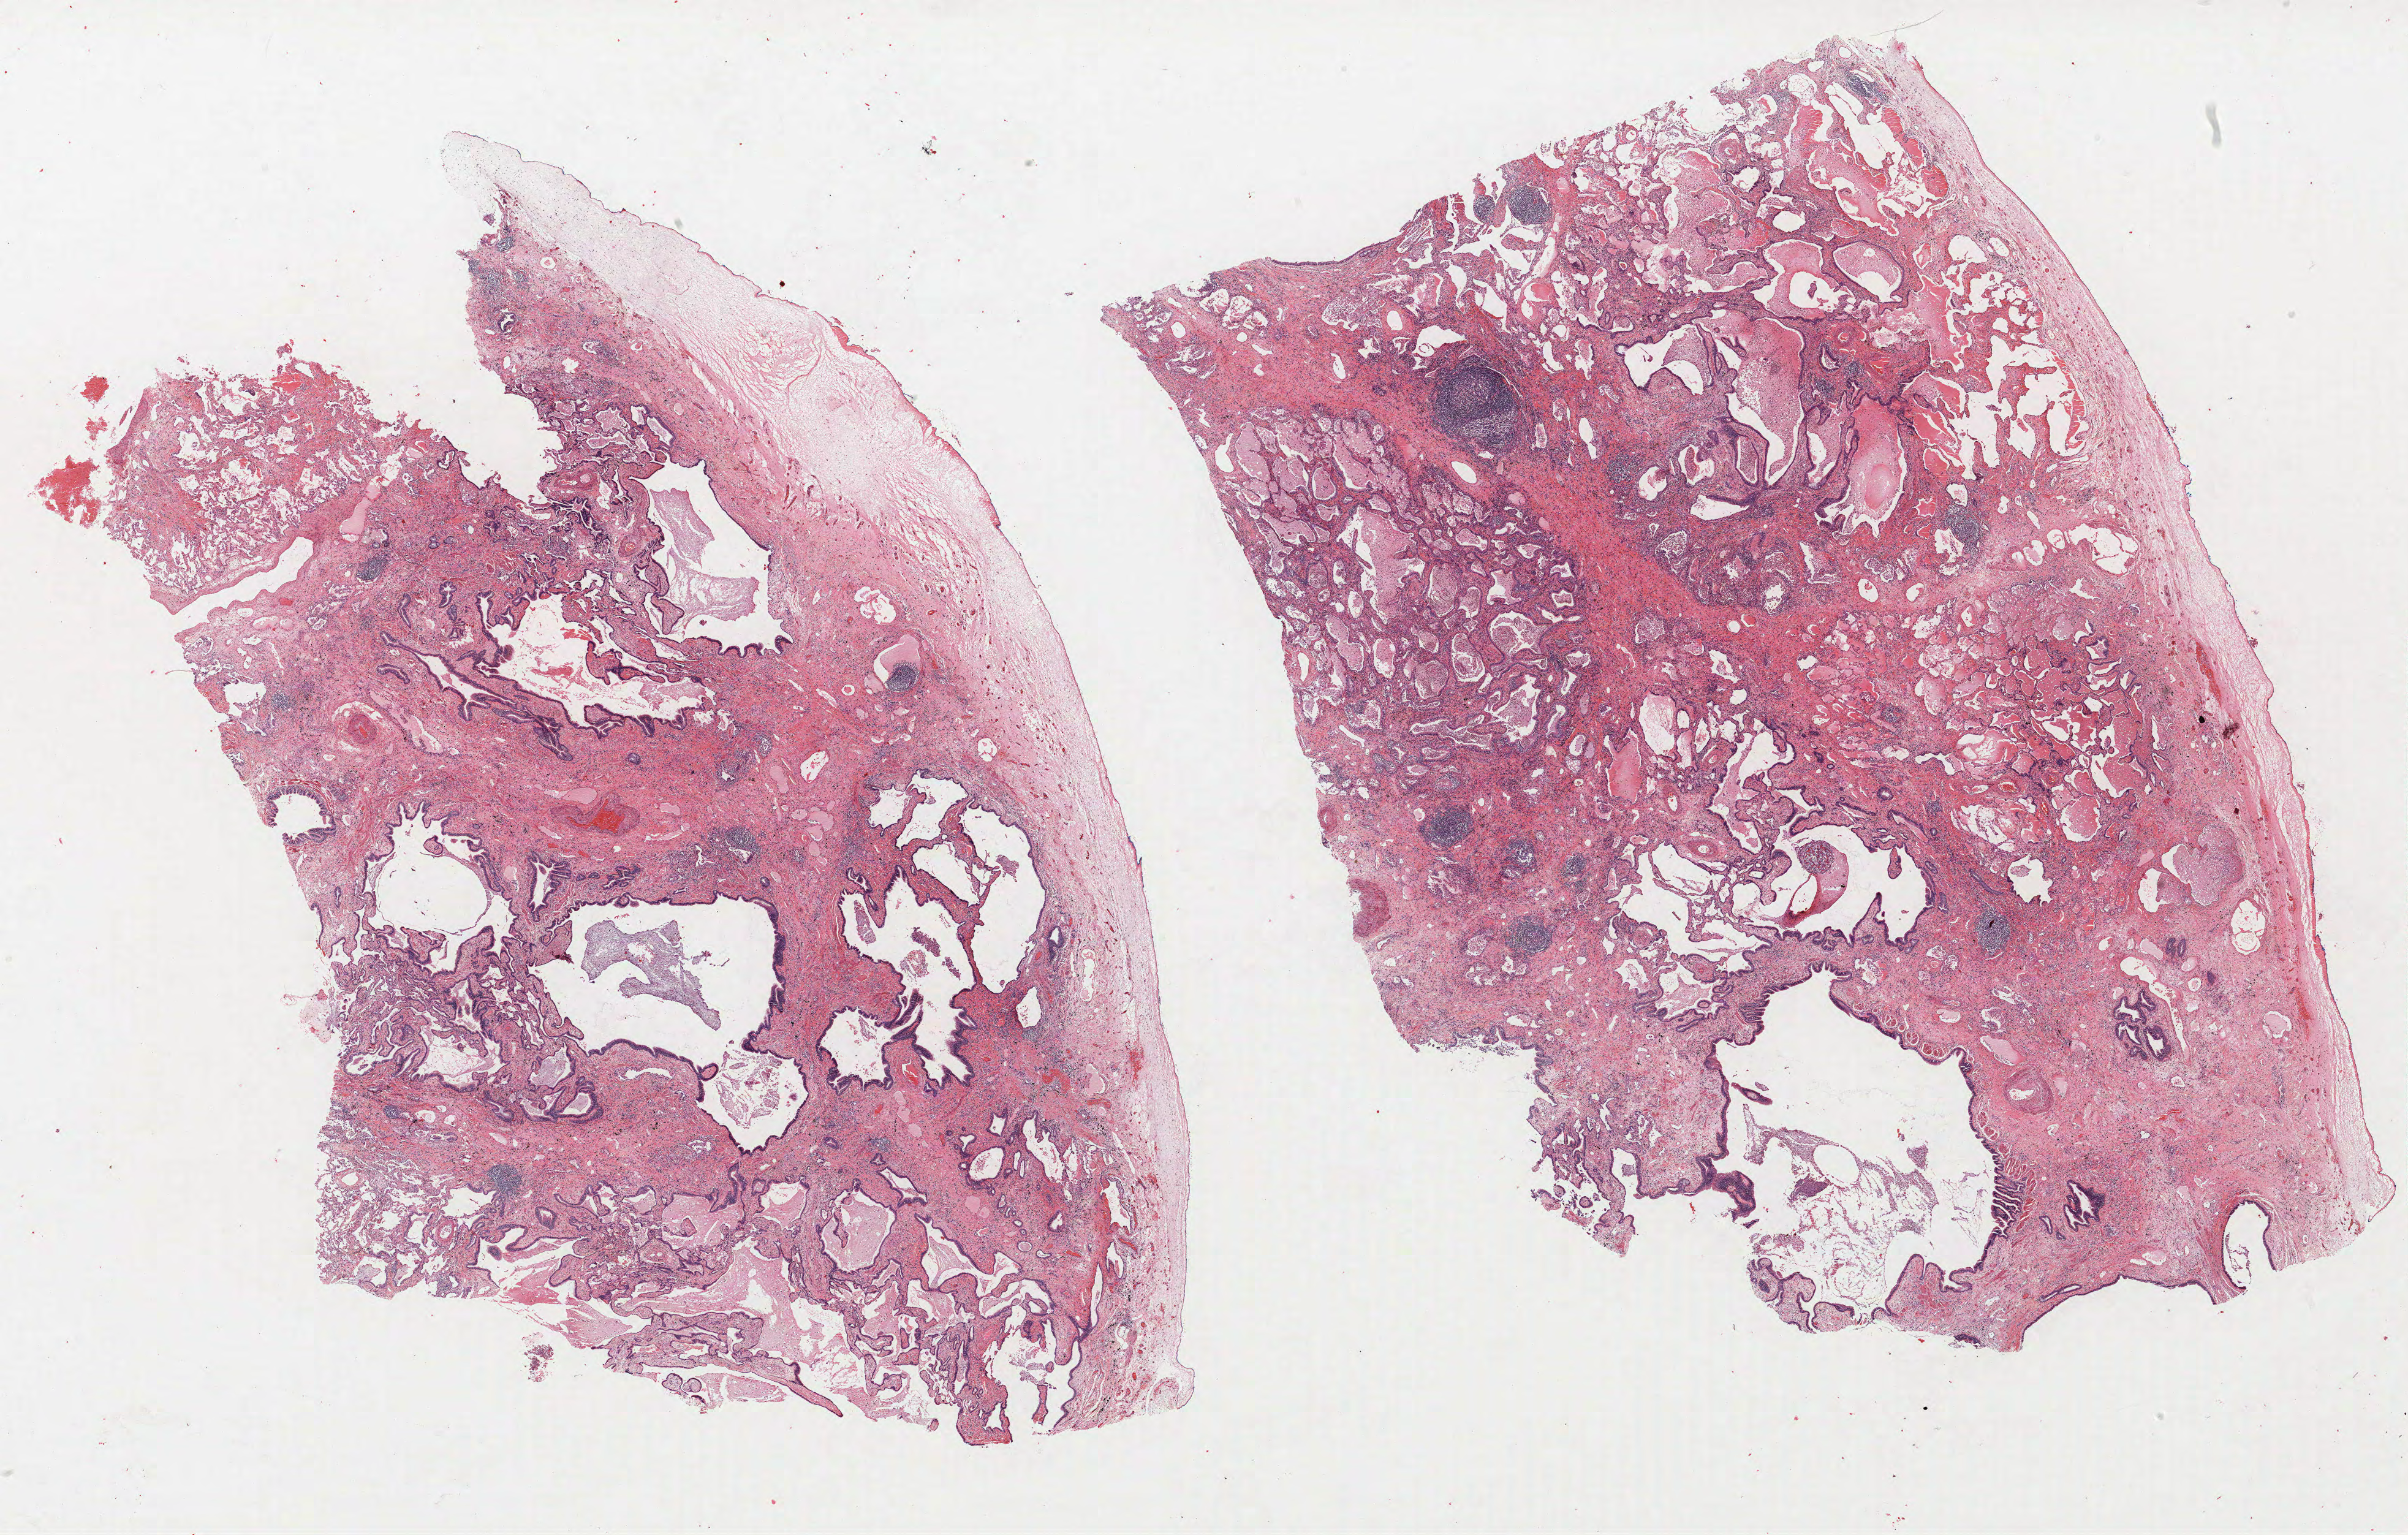
Whole-slide histology image, H&E, low-resolution overview of the scanned area, about 31.4 x 20.0 mm (slide scanned at 40x); FFPE section; lung. Male patient, aged 58 at enrolment. Current smoker at enrolment. Grade: moderately differentiated (G2).
Tumour size (pathology): 38 mm. Primary tumour location (clinical record): right lower lobe. Stage (AJCC 6th edition): IB. Participant's lung-cancer diagnosis: Squamous cell carcinoma, keratinizing, NOS (ICD-O-3 8071/3). Note: participant had 2 primary lung cancers recorded; fields above describe the first.